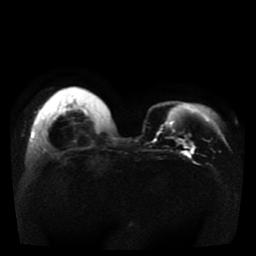
Breast MRI, one axial slice. Position 11 of 41 along the scan axis. Diffusion-weighted series; image 2 of 4 stored at this slice position (different b-values; order by instance number). 1.5 T. 5 mm slice thickness. 256 × 256 image matrix, field of view 330 × 330 mm. Female patient.
Outlined on this slice (manually delineated by an expert):
- tumour on diffusion-weighted imaging: bounding box <176,139,183,145> (left, top, right, bottom; pixels)